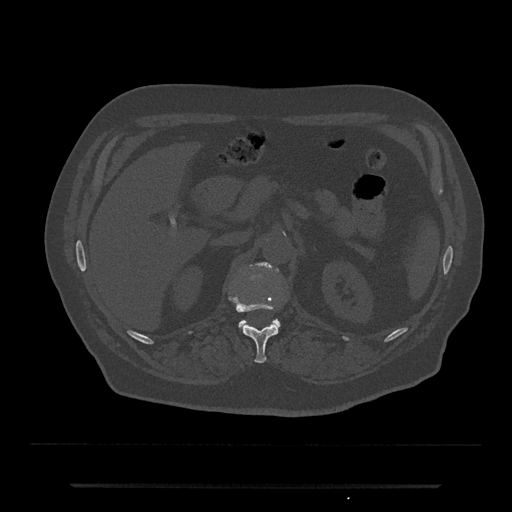
CT including the spine, one axial slice; position 575 of 797 along the scan axis; reconstruction kernel Br40s/3; 120 kVp; bone window (W 1800 / L 400 HU); 512 × 512 image matrix. Patient: male, 80 years. Case-level facts recorded for this patient, not image findings: primary cancer: prostate.
Outlined on this slice (semi-automatic segmentation, software-assisted and operator-edited):
- L1 vertebra: bounding box (x1, y1, x2, y2) in pixels: (239, 262, 281, 329)
- T12 vertebra: (230, 297, 279, 363)